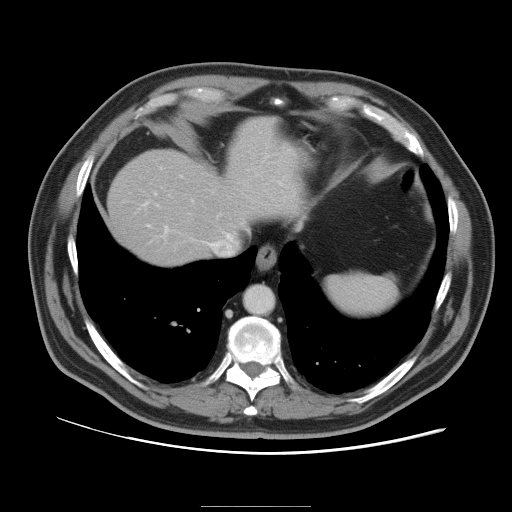
Contrast-enhanced abdominal CT, one axial slice; slice 86 of 105 in the series (ordered by position); 120 kVp; intravenous contrast given; soft-tissue window (W 400 / L 40 HU); 5 mm slice thickness; 512 × 512 image matrix. Male patient, age 64 years. From the clinical record (not read from this slice): diagnosis: colorectal cancer liver metastases, imaged before liver resection; multiple liver metastases: yes; largest metastasis: 3 cm; chemotherapy before resection: yes.
Outlined on this slice (expert manual segmentation):
- hepatic veins: box from (x=147, y=194) to (x=234, y=240) px
- liver: (x=108, y=117)–(x=299, y=265)
- planned liver remnant (the part of the liver to remain after resection): (x=108, y=155)–(x=230, y=265)
- portal vein (with intrahepatic branches): (x=142, y=175)–(x=194, y=238)